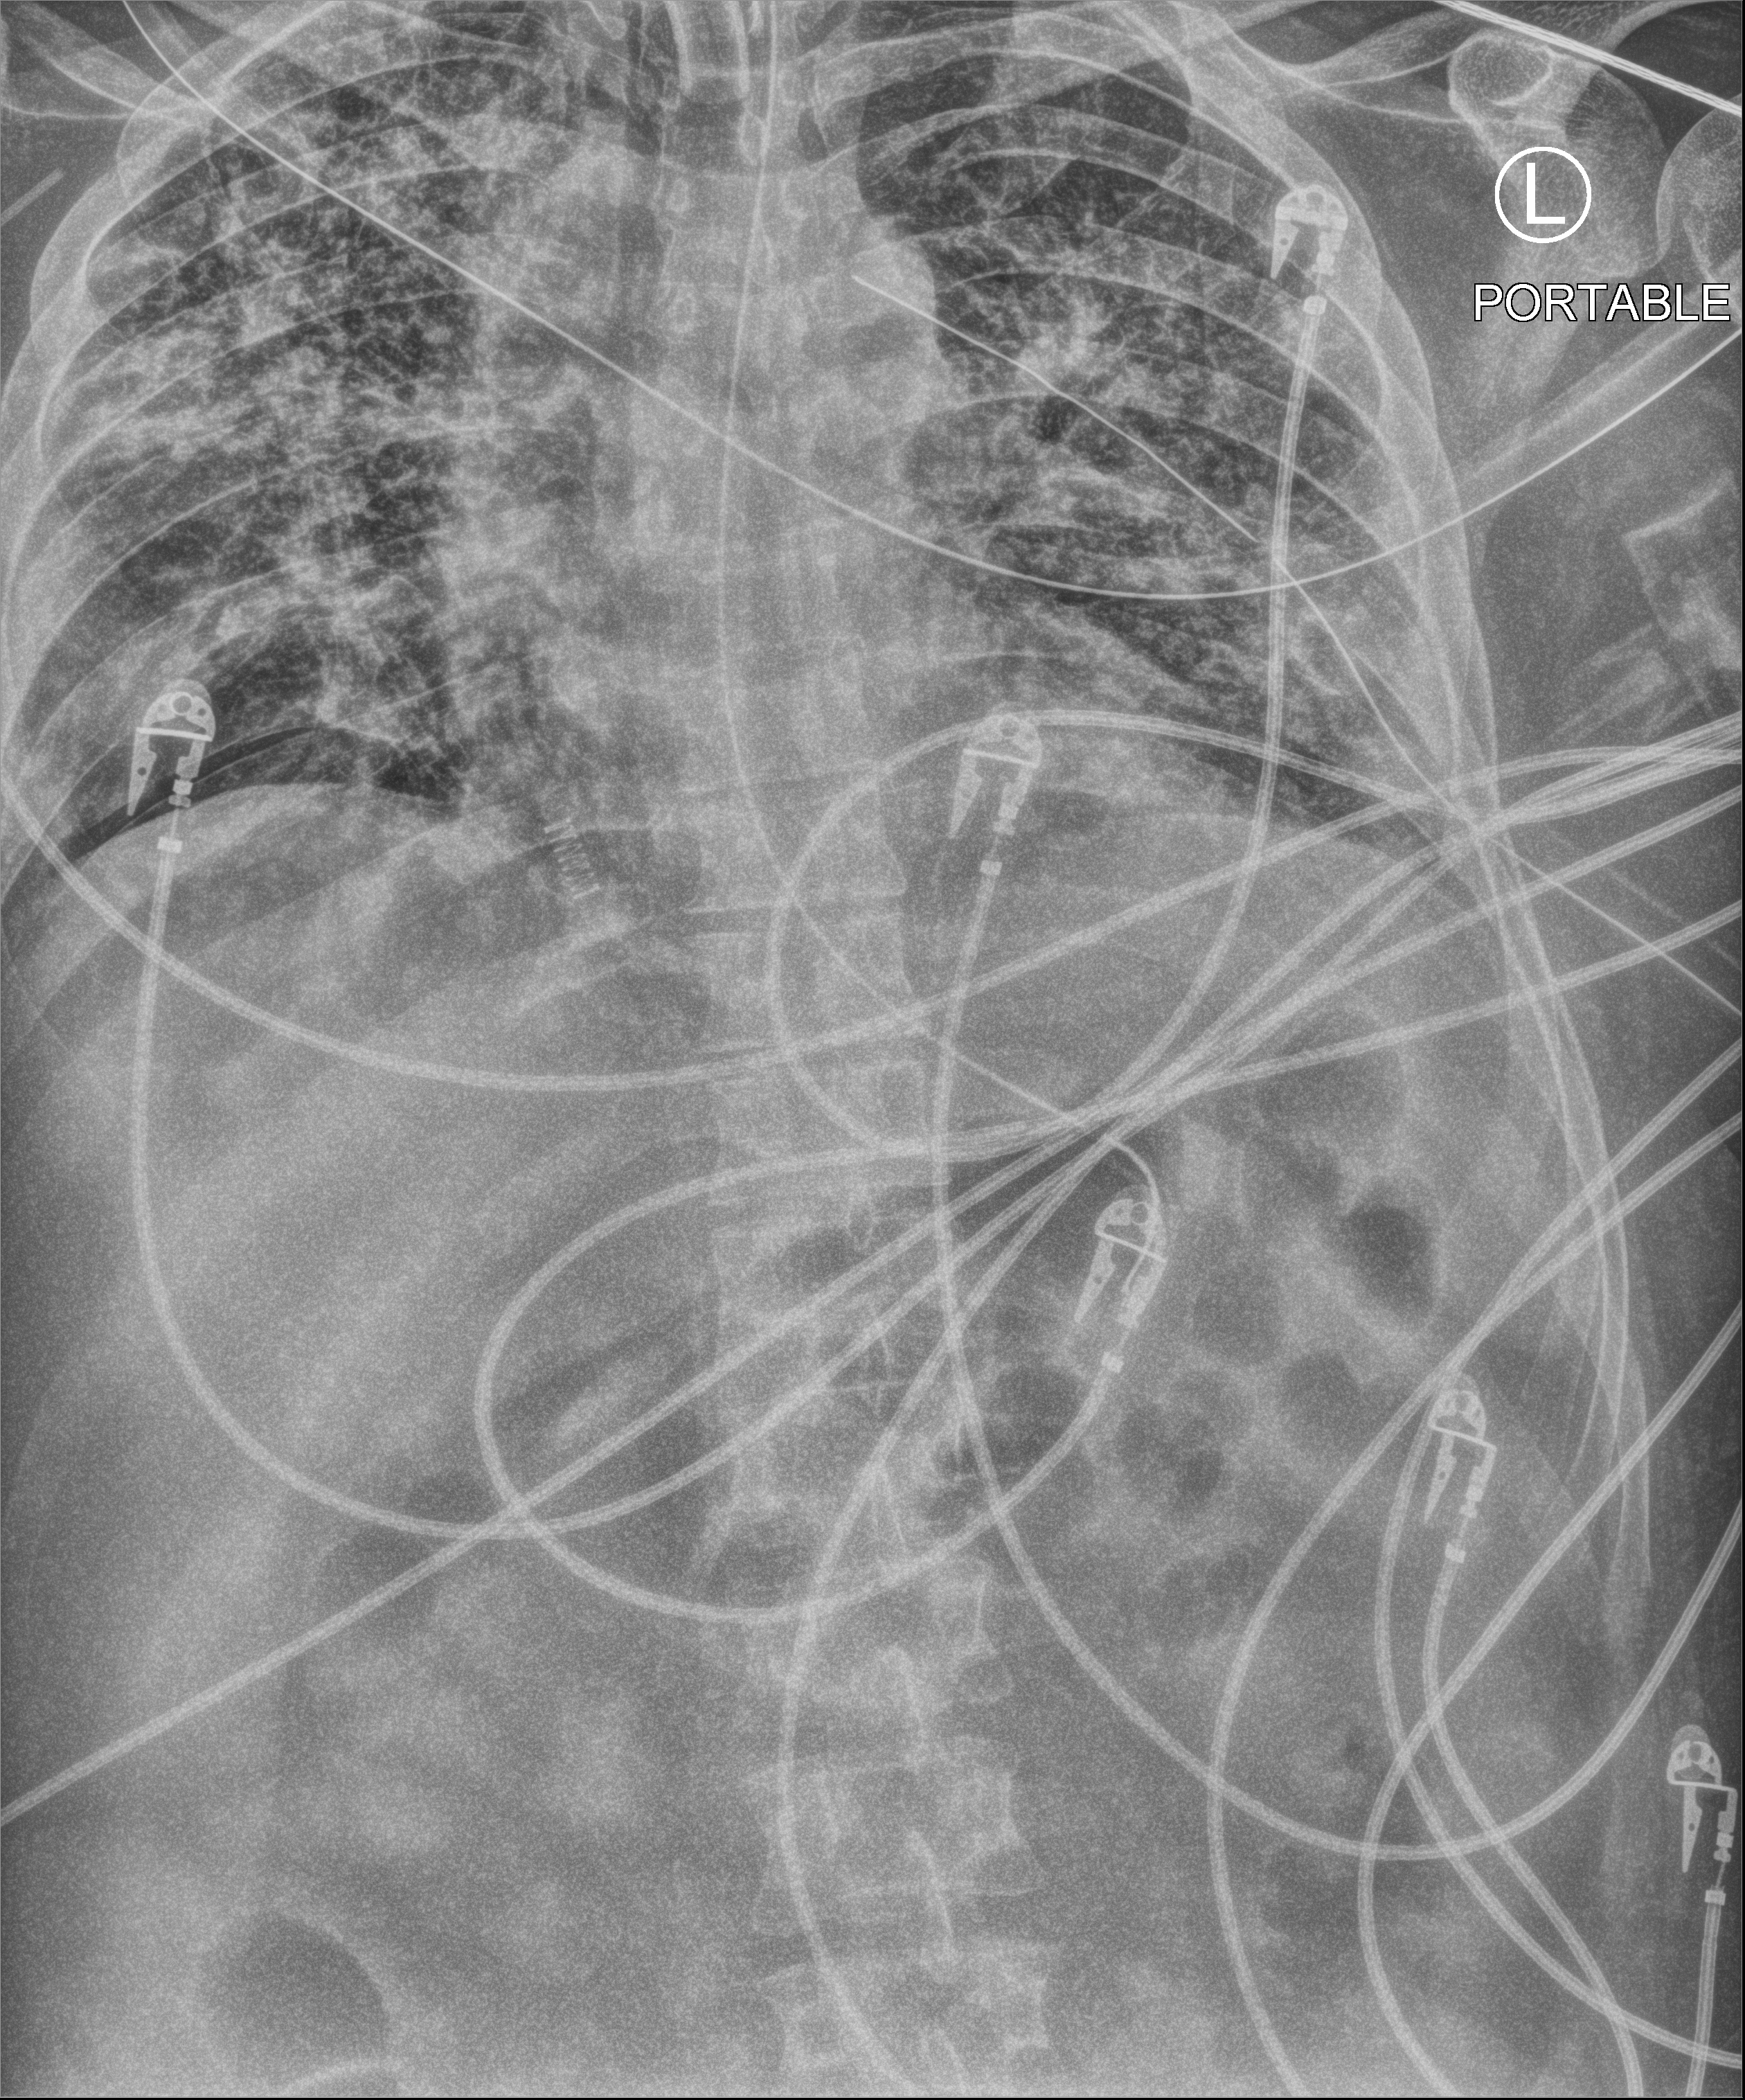
Portable chest radiograph. Male patient hospitalised with COVID-19, age 18–59 years.
Hospital-stay facts (about this admission, not read from this image; timing relative to this image not recorded):
- length of hospital stay: 63 days